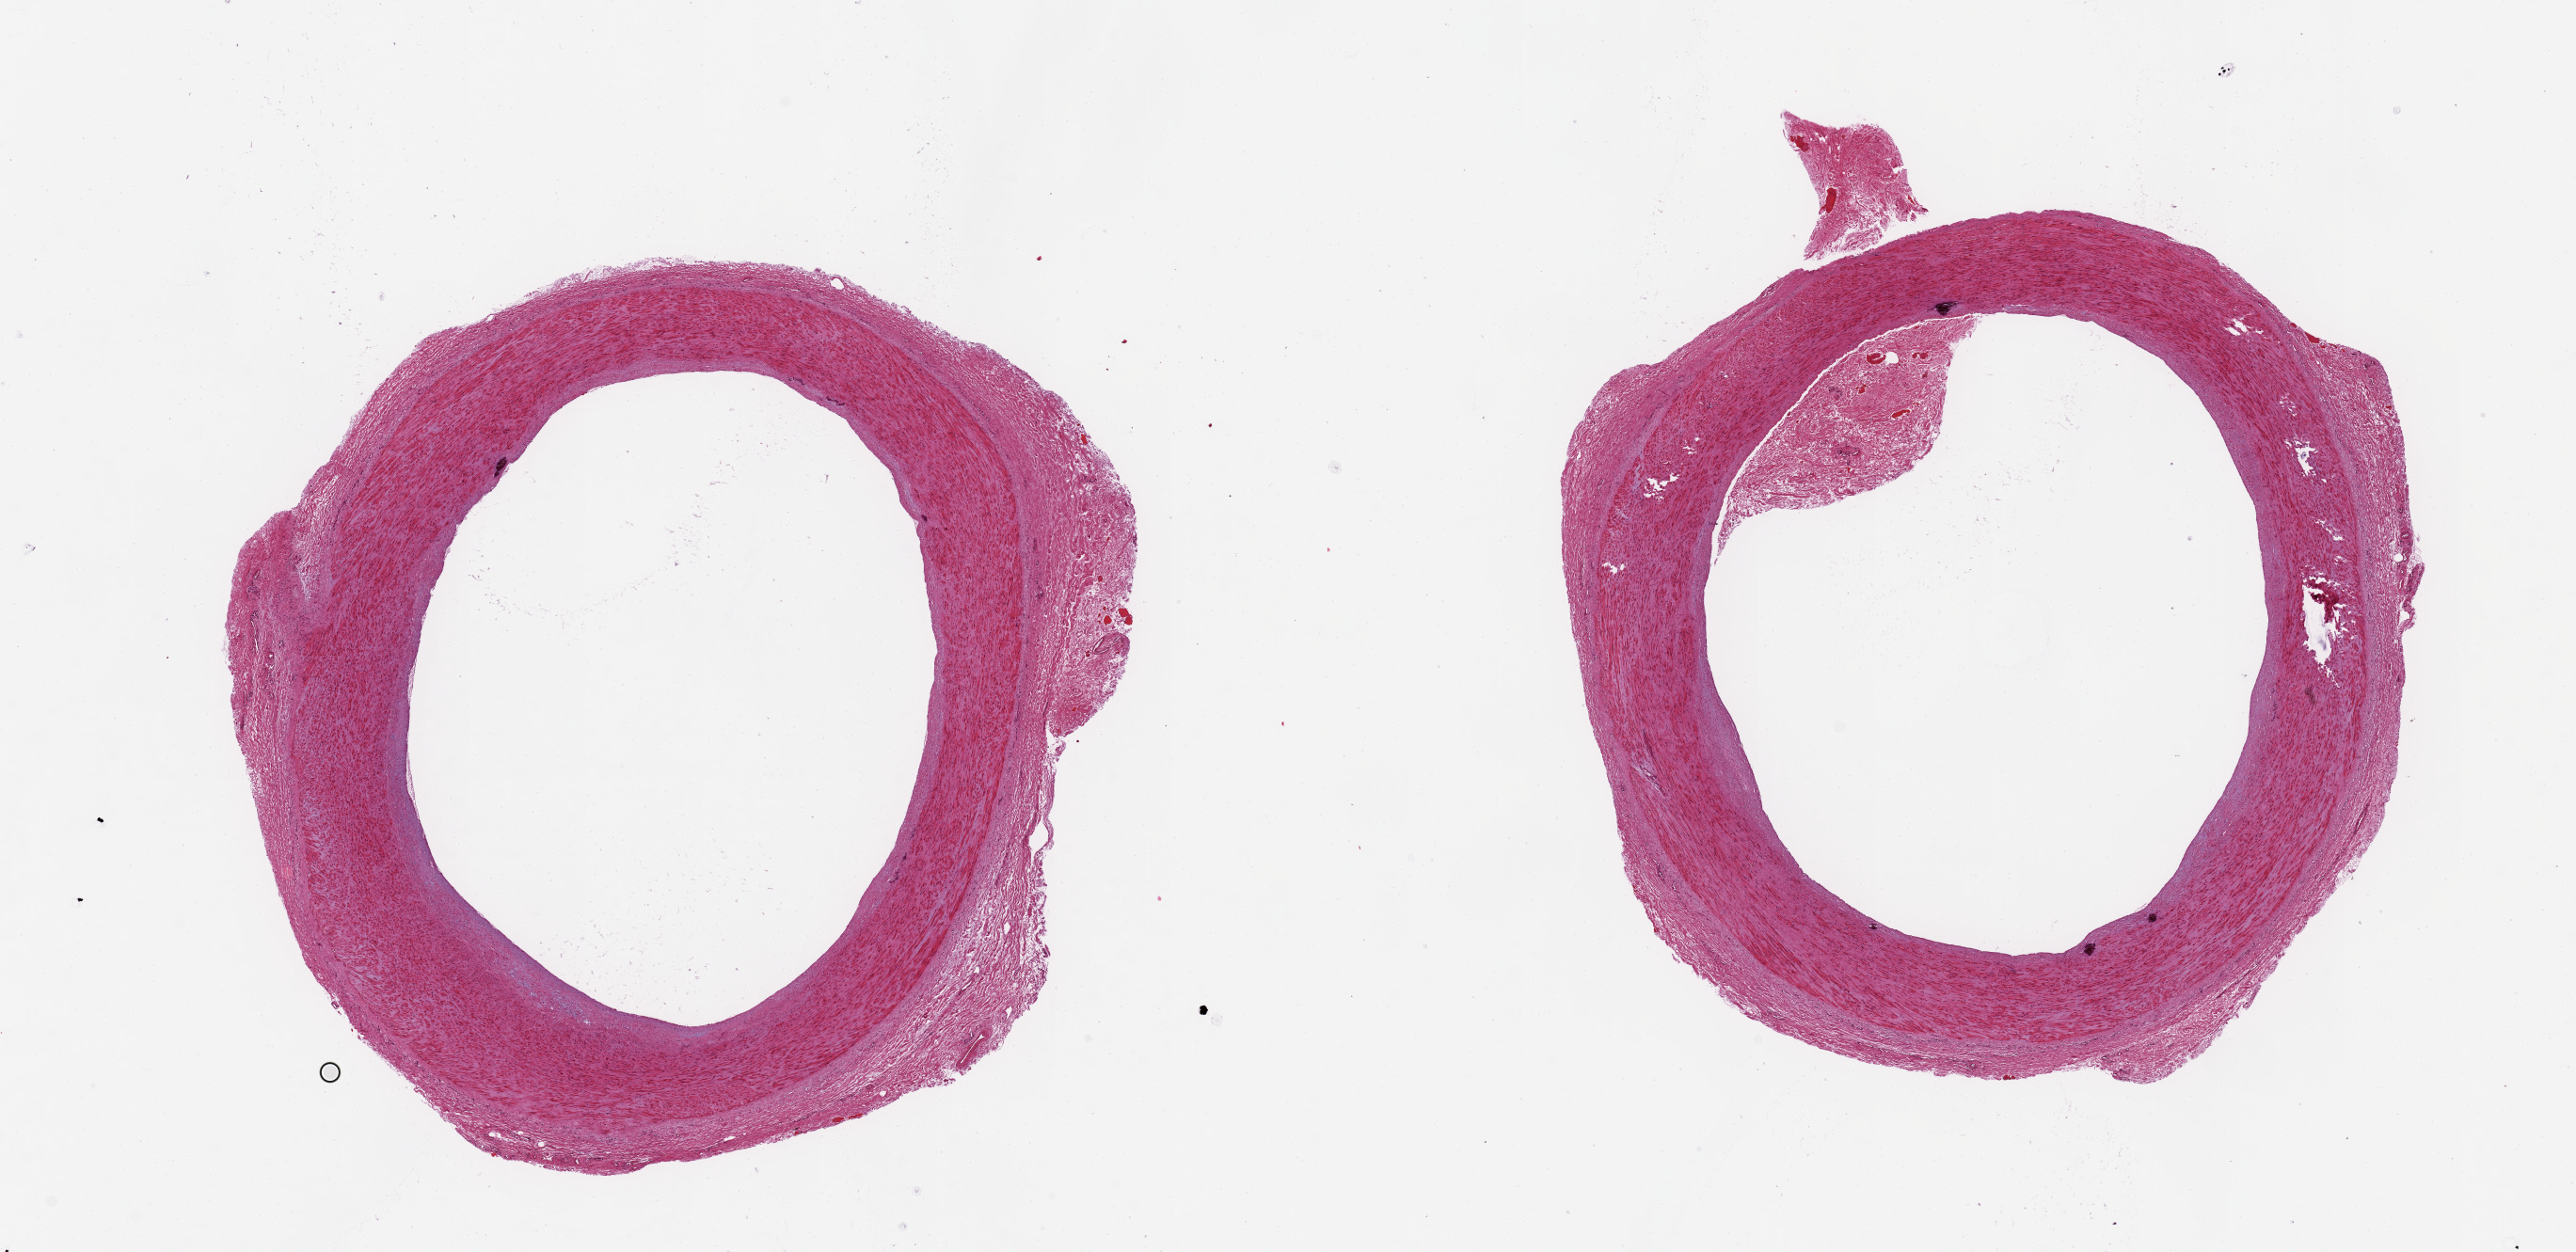
H&E whole-slide image — whole scanned area (about 21.7 x 10.5 mm) shown as a low-resolution overview, PAXgene-fixed paraffin-embedded (PFPE) section, section of tibial artery (target tissue), tissue donor sample. Donor: male.
• reviewer comment on this tissue sample: Good, clean specimen